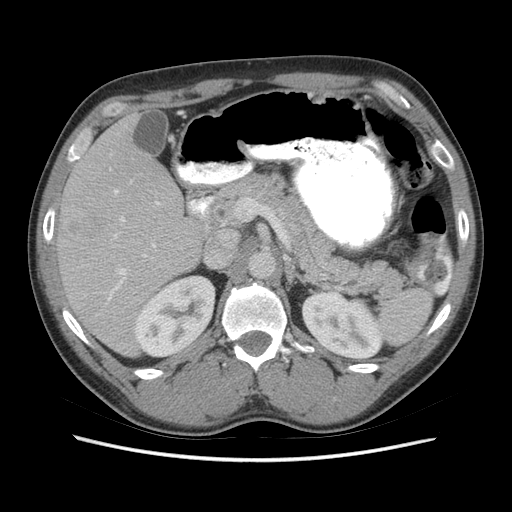
Contrast-enhanced abdominal CT (liver protocol), one axial slice; 140 kVp; soft-tissue window (W 400 / L 40 HU); 2.5 mm slice thickness; 512 × 512 image matrix, field of view 360 × 360 mm. Case-level facts recorded for this patient, not image findings: diagnosis: hepatocellular carcinoma (patient treated with transarterial chemoembolisation; whether this scan precedes or follows treatment is not stated here); TNM stage (as recorded): Stage-IIIA; Child-Pugh class: A; tumour nodularity: multinodular; tumour size: 6.6 cm.
Annotated regions visible in this slice (semi-automatic segmentation, software-assisted and operator-edited):
- liver parenchyma outside the tumour (the mass and vessels are separate outlines, so this box may not span the whole liver): box from (x=56, y=114) to (x=217, y=356) px
- mass: (x=67, y=217)–(x=98, y=241)
- liver vessels: (x=108, y=190)–(x=160, y=300)